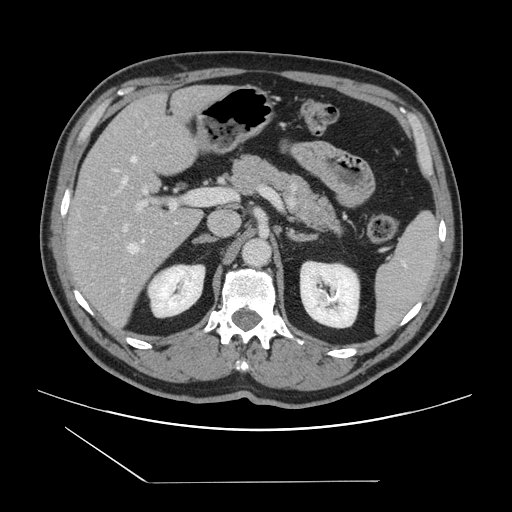
Contrast-enhanced abdominal CT, one axial slice. Slice 82 of 157 in the series (ordered by position). 120 kVp. Intravenous contrast given. Soft-tissue window (W 400 / L 40 HU). 2.5 mm slice thickness. 512 × 512 image matrix, field of view 407 × 407 mm. Male patient, age 61 years. From the clinical record (not read from this slice): diagnosis: colorectal cancer liver metastases, imaged before liver resection; multiple liver metastases: yes; largest metastasis: 5.5 cm.
Outlined on this slice (outlined manually by an expert reader):
- hepatic veins: box from (x=114, y=157) to (x=144, y=282) px
- liver: (x=67, y=86)–(x=226, y=333)
- planned liver remnant (the part of the liver to remain after resection): (x=67, y=86)–(x=225, y=221)
- portal vein (with intrahepatic branches): (x=105, y=188)–(x=206, y=231)